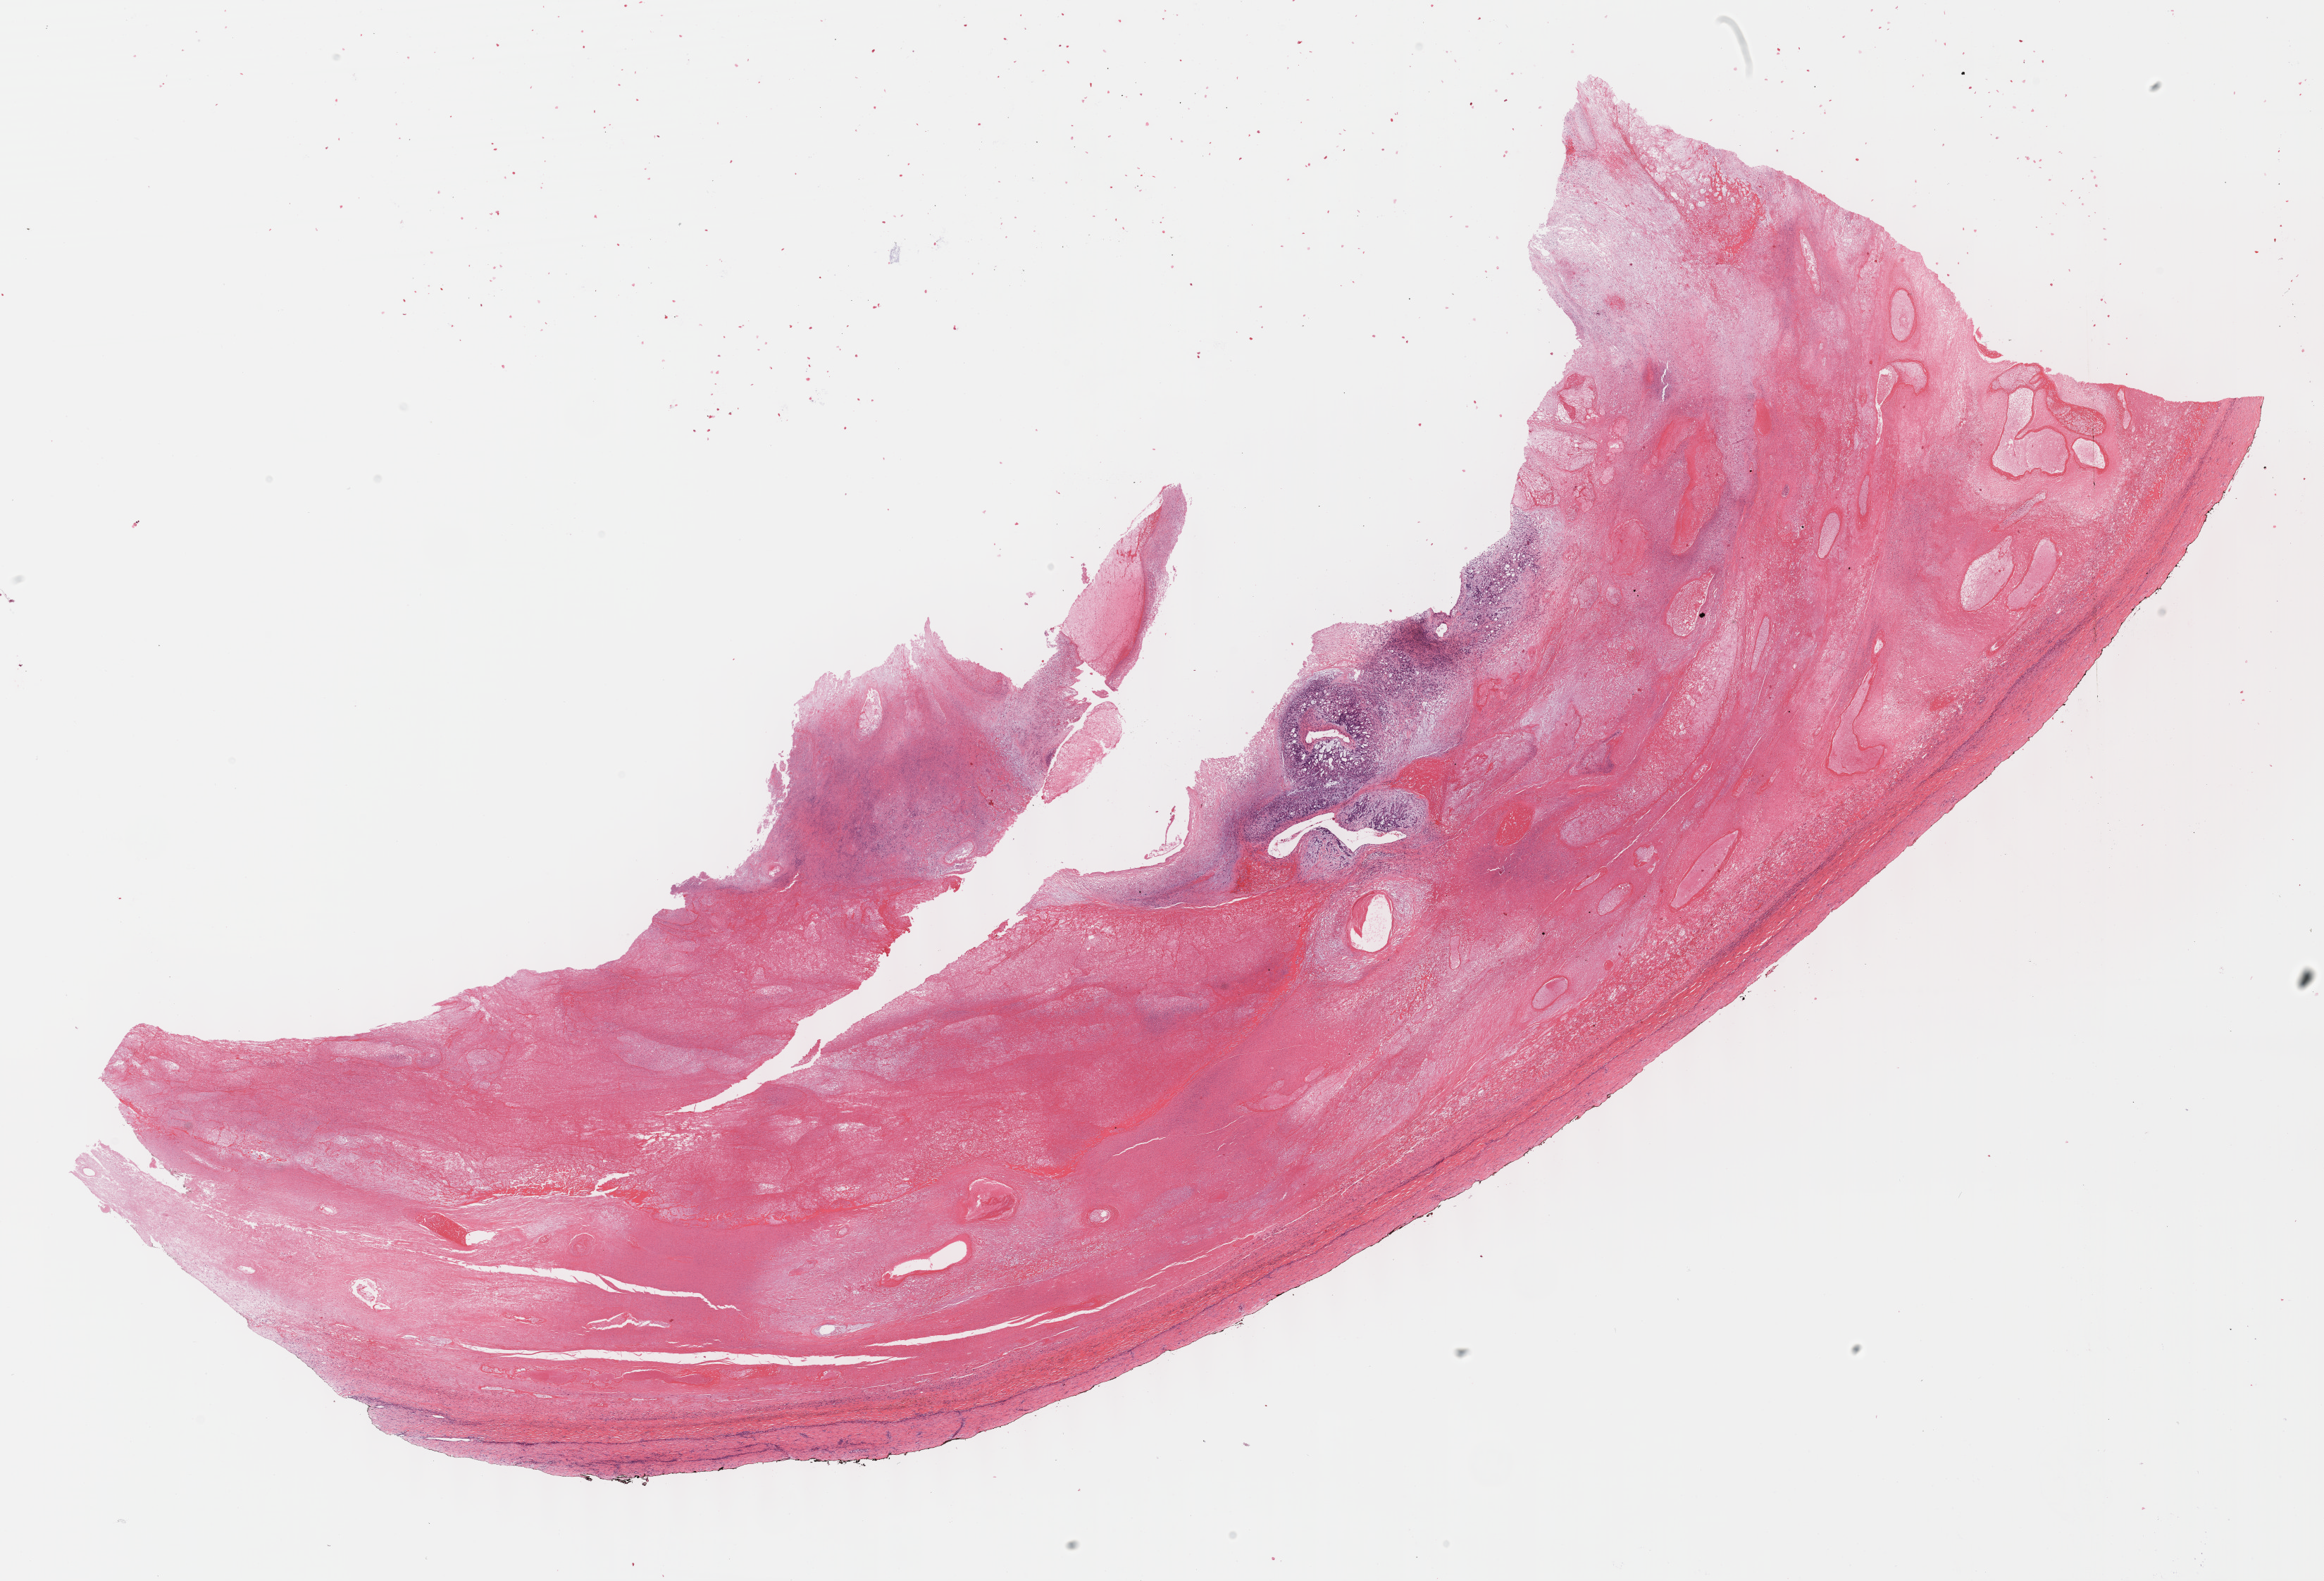
H&E whole-slide image — shown as a low-resolution overview of the whole scanned area (about 26.7 x 18.1 mm, from a 40x scan); formalin-fixed paraffin-embedded (FFPE) diagnostic section; mesothelium, primary tumour sample. Patient: male, age at initial diagnosis 61 years.
AJCC pathologic stage: I. Laterality: right. Diagnosis: Mesothelioma, biphasic, malignant (pleura, NOS). TNM: T1 N0 MX.